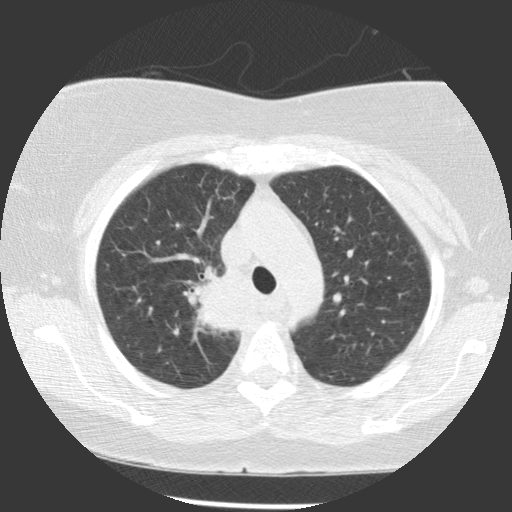
Low-dose screening chest CT, one axial slice. Position 86 of 116 along the scan axis. 140 kVp. Lung window (W 1500 / L -600 HU). 512 × 512 image matrix, field of view 320 × 320 mm.
Outlined on this slice (outlined manually by an expert reader):
- lesion 1 (tumor, upper lobe of right lung): bounding box (x1, y1, x2, y2) in pixels: (189, 266, 244, 336)